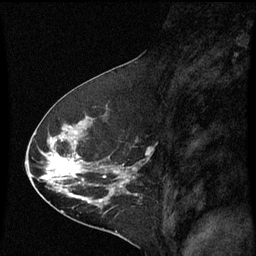
Breast MRI (dynamic contrast-enhanced), one sagittal slice. Slice 31 of 60 in the series (ordered by position). Dynamic contrast-enhanced series, image 2 of 3 at this slice position (ordered by acquisition). 1.5 T. TE 4.2 ms, TR 8.9 ms. 256 × 256 image matrix, field of view 200 × 200 mm. Patient: female, 53 years. Case-level facts recorded for this patient, not image findings: setting: breast cancer imaged before/during neoadjuvant chemotherapy; receptor status: HR-positive, HER2-negative.
Outlined on this slice (semi-automatic segmentation, software-assisted and operator-edited):
- analysis volume of interest (the breast-tissue region the enhancement analysis was run in; not a lesion): bounding box (x1, y1, x2, y2) in pixels: (32, 100, 143, 221)
- tumour enhancement mask (voxels above the 70 % enhancement threshold inside the analysis volume of interest): (46, 156, 127, 201)